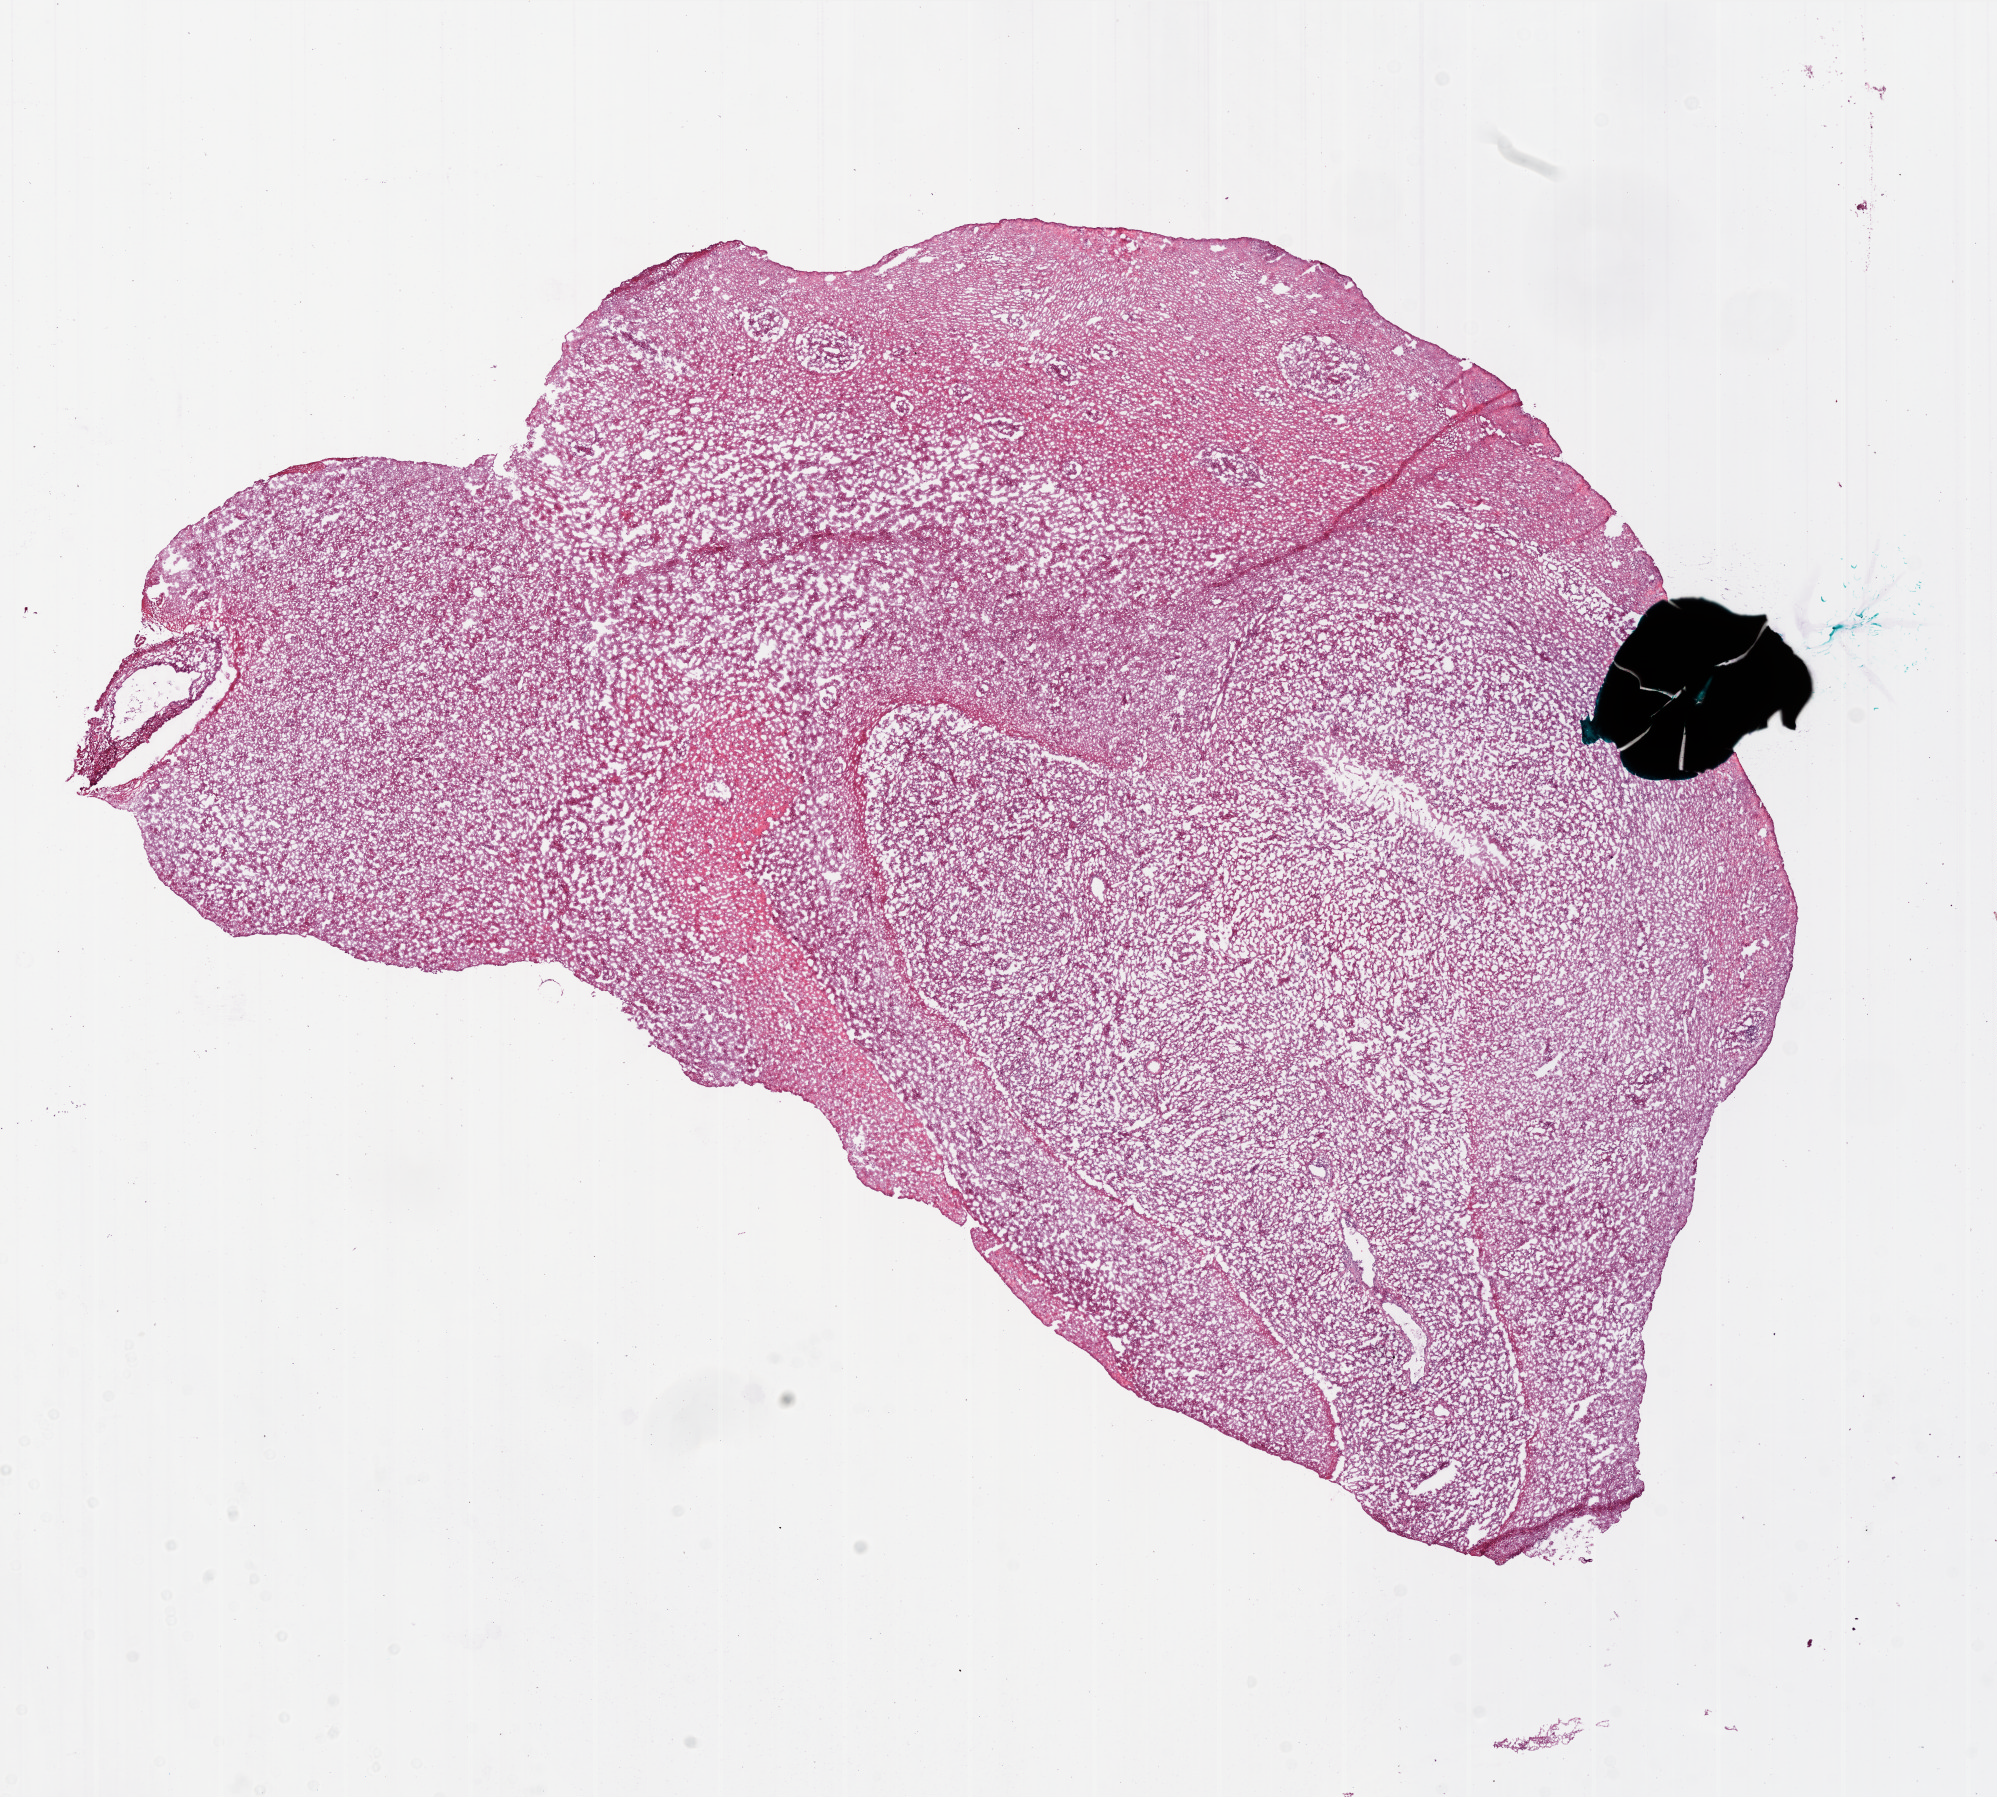
Digitized H&E tissue section (whole slide), a low-resolution overview of the entire scanned area, about 16.0 x 14.4 mm (from a 20x scan), frozen section from the bottom of the tissue portion, sample: primary tumour, brain. Female patient; age at initial diagnosis 82 years. Pathologist review of this section (percent, as recorded): tumour cells 60%, tumour nuclei 80%, normal cells 0%, stromal cells 35%, necrosis 5%. Infiltration values recorded for this section: lymphocyte infiltration 0%.
Histologic diagnosis: Glioblastoma.